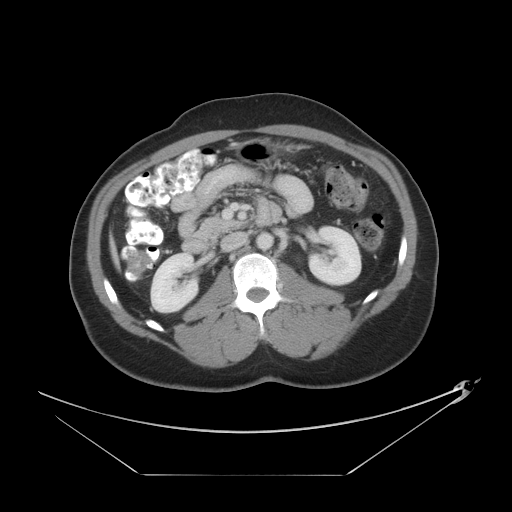
Contrast-enhanced abdominal CT, one axial slice. Position 15 of 44 along the scan axis. Reconstruction kernel STANDARD. Intravenous contrast given. Soft-tissue window (W 400 / L 40 HU). 5 mm slice thickness. 512 × 512 image matrix, field of view 466 × 466 mm. Male patient, age 49 years. Case-level facts recorded for this patient, not image findings: diagnosis: colorectal cancer liver metastases, imaged before liver resection; multiple liver metastases: no; largest metastasis: 8.5 cm; disease in both lobes: yes.
Structures marked on this image (expert manual segmentation):
- liver: bounding box <109,236,119,265> (left, top, right, bottom; pixels)